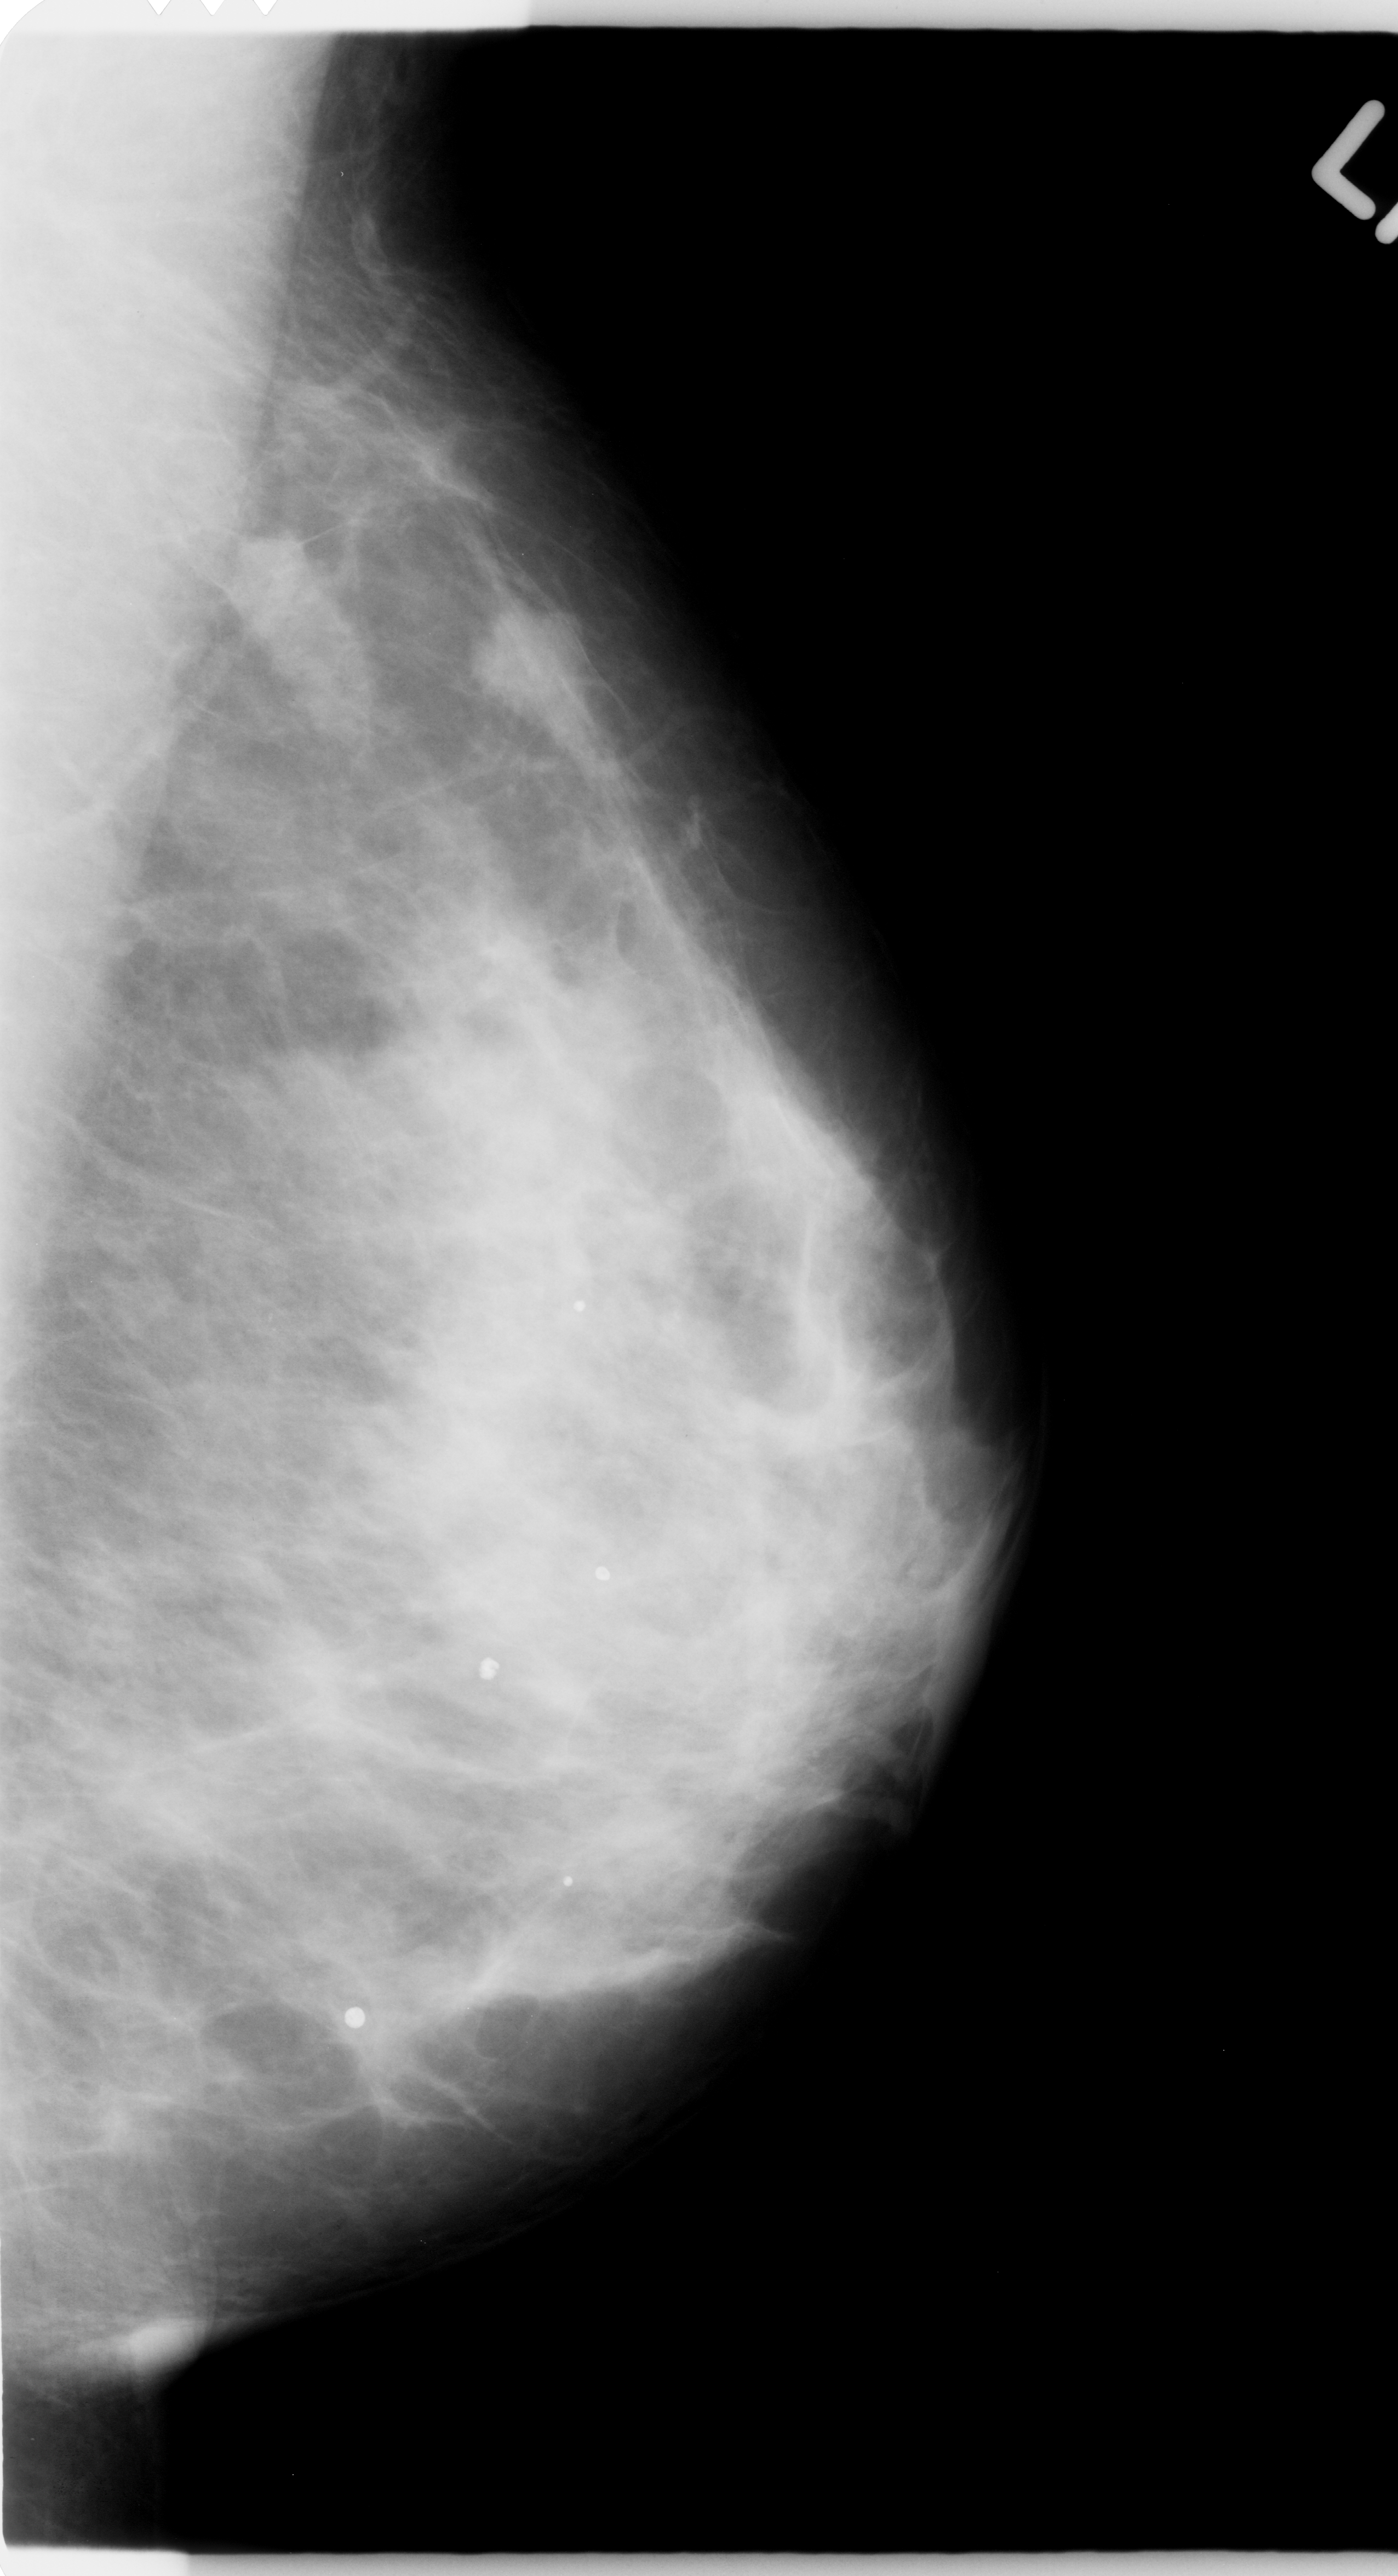
Mammogram (digitized film), left breast, mediolateral oblique (MLO) view, breast composition: heterogeneously dense (BI-RADS density category 3 of 4).
Abnormality record for this image: mass, shape lobulated, margins microlobulated; BI-RADS assessment category 4; subtlety rating 5 on a 1 (subtle) to 5 (obvious) scale; pathology result (as recorded, not read from the image): malignant.